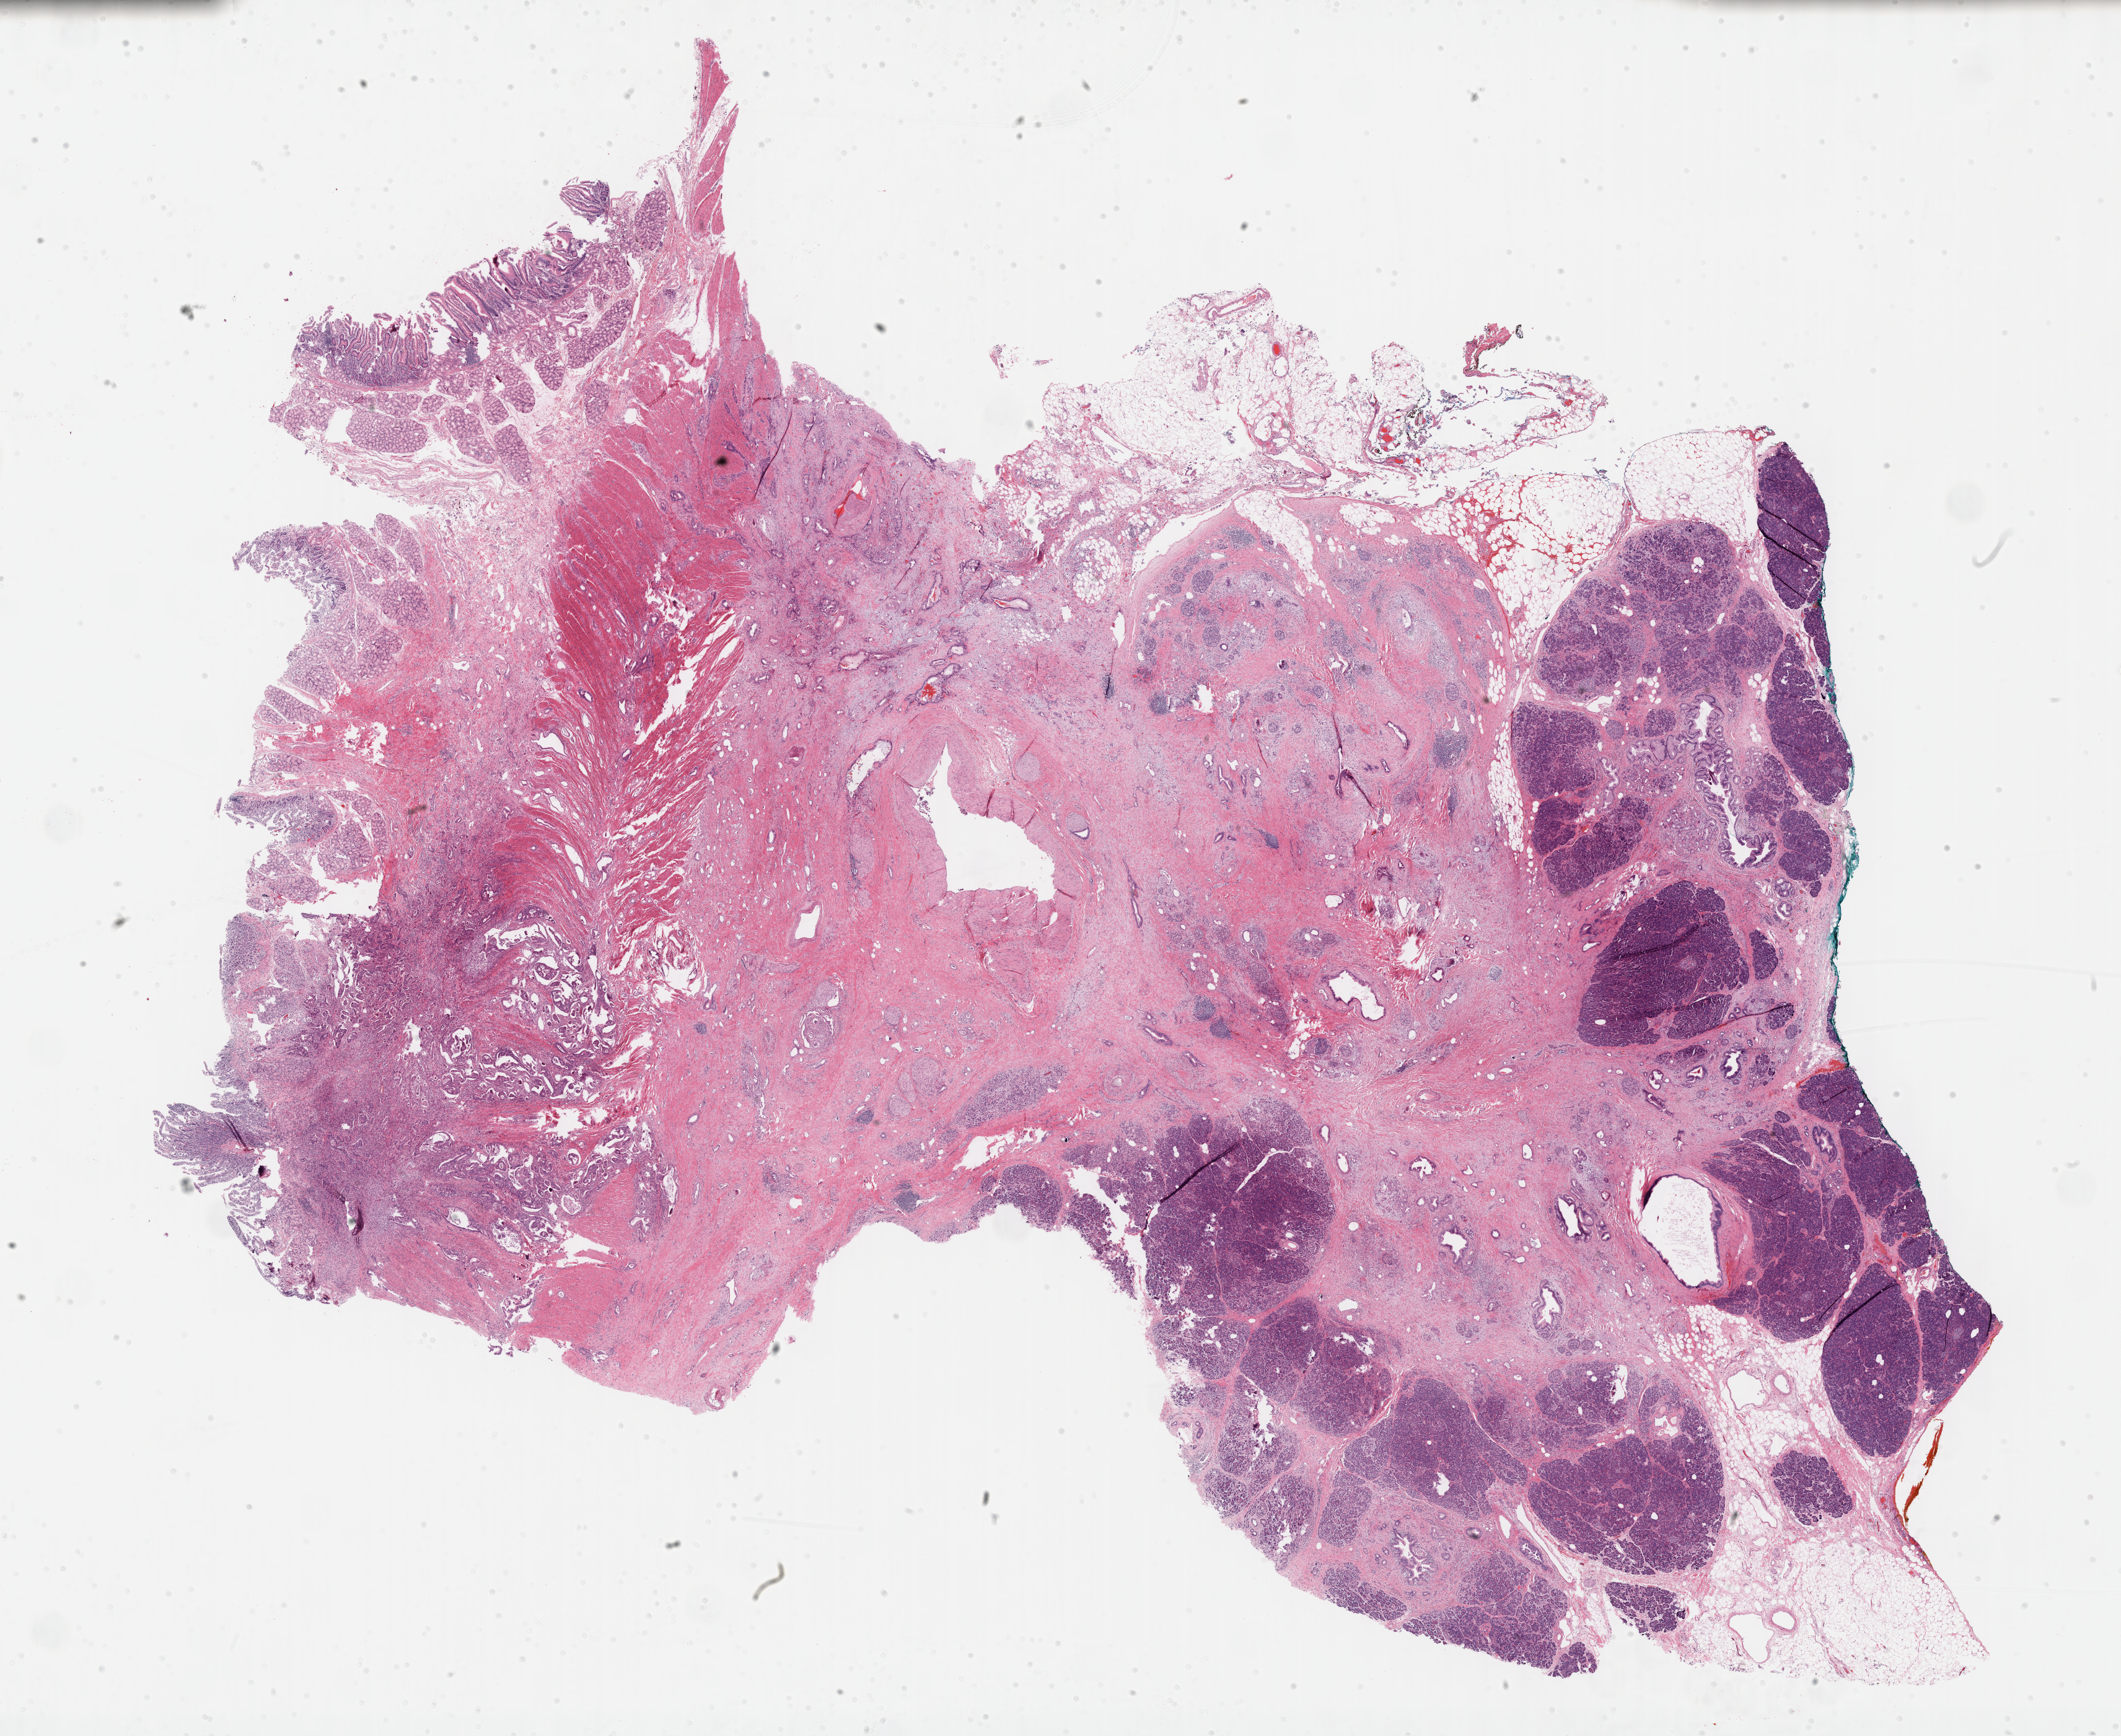
Digitized Hematoxylin and eosin (H&E) stained tissue section (whole slide), low-resolution overview of the scanned area, about 27.7 x 22.7 mm (from a 40x scan). FFPE section. Pancreas, primary tumour sample. Patient: female, age at initial diagnosis 57 years. Histologic grade: G2 (moderately differentiated).
Histologic diagnosis: Infiltrating duct carcinoma, NOS (head of pancreas). AJCC pathologic stage: IIB (7th edition).